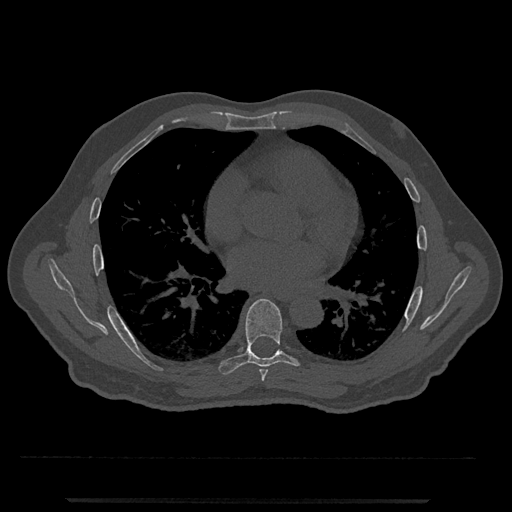
CT including the spine, one axial slice. Position 690 of 797 along the scan axis. Reconstruction kernel Br40s/3. 120 kVp. Bone window (W 1800 / L 400 HU). 512 × 512 image matrix, field of view 419 × 419 mm. Patient: male, 63 years. Case-level facts recorded for this patient, not image findings: primary cancer: prostate.
Structures marked on this image (semi-automatically segmented with operator editing):
- T6 vertebra: bounding box (x1, y1, x2, y2) in pixels: (259, 369, 268, 381)
- T7 vertebra: (218, 299, 304, 375)